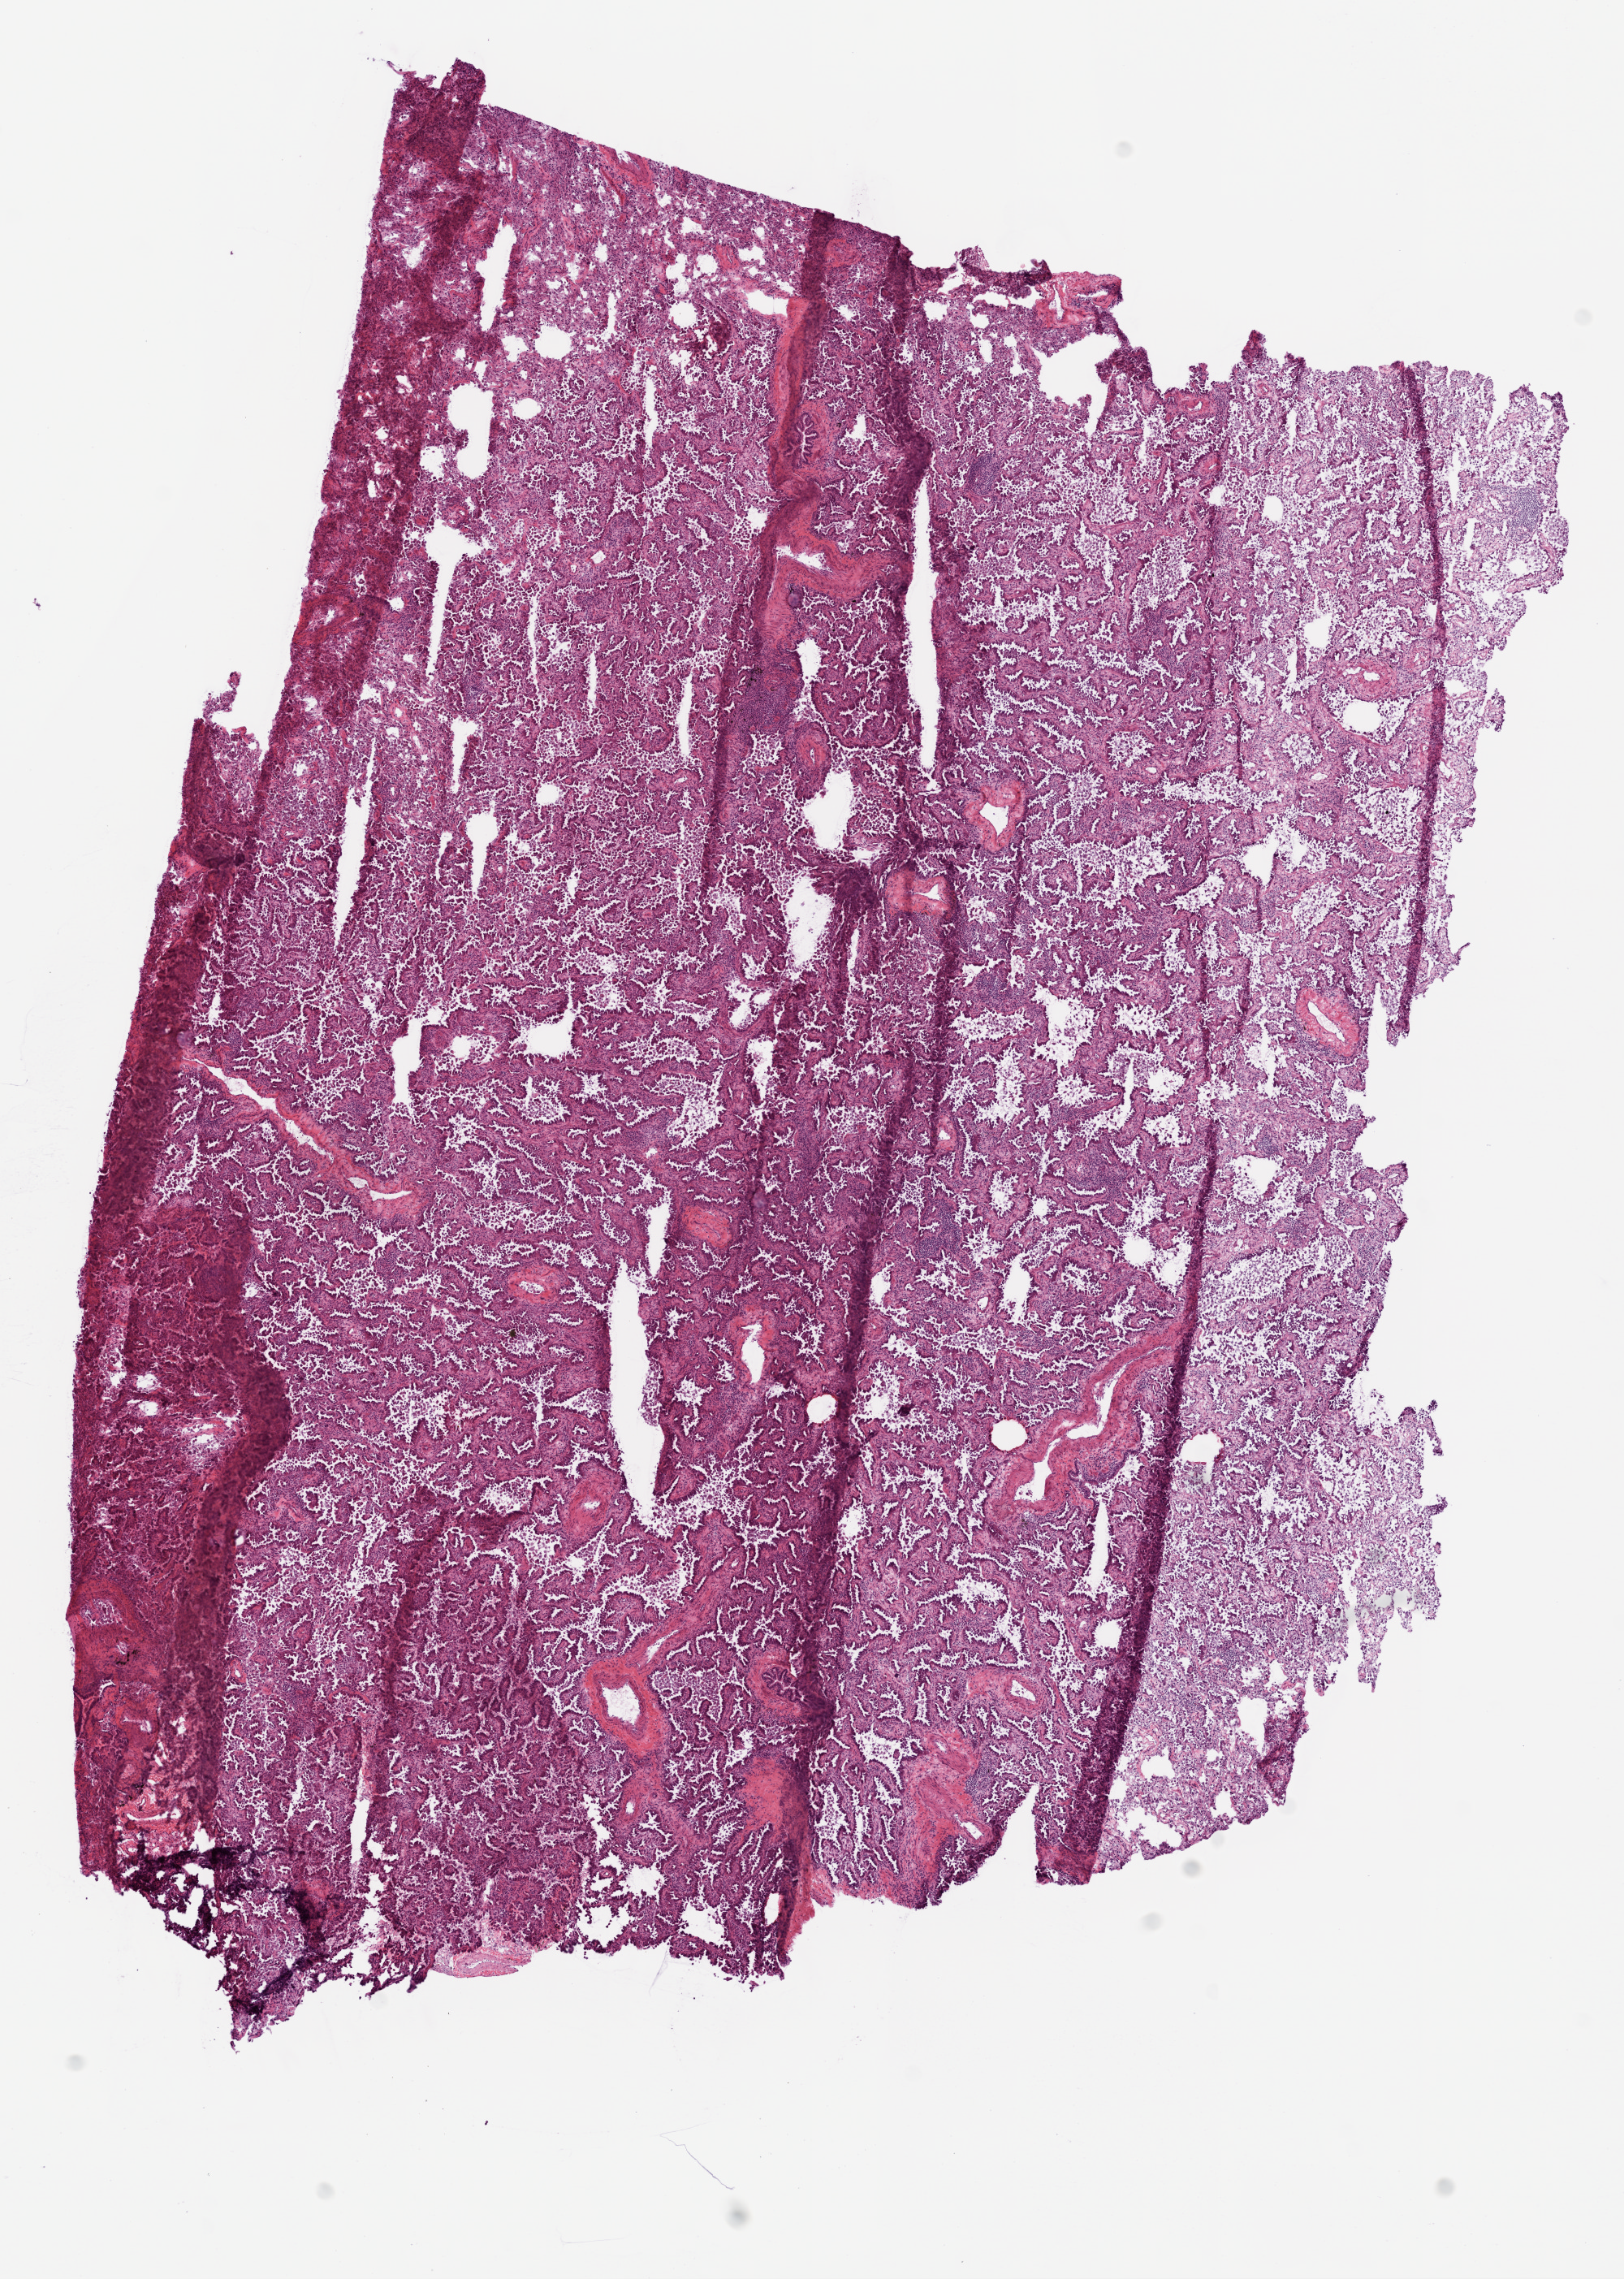
Whole-slide histology image, H&E, a low-resolution overview of the entire scanned area, about 8.0 x 11.3 mm (from a 20x scan), frozen section, lung, primary tumour sample. Female patient; age at initial diagnosis 55 years. Pathologist review of this section (percent, as recorded): tumour cells 100%, tumour nuclei 80%.
Diagnosis: Bronchiolo-alveolar carcinoma, non-mucinous (lower lobe, lung).